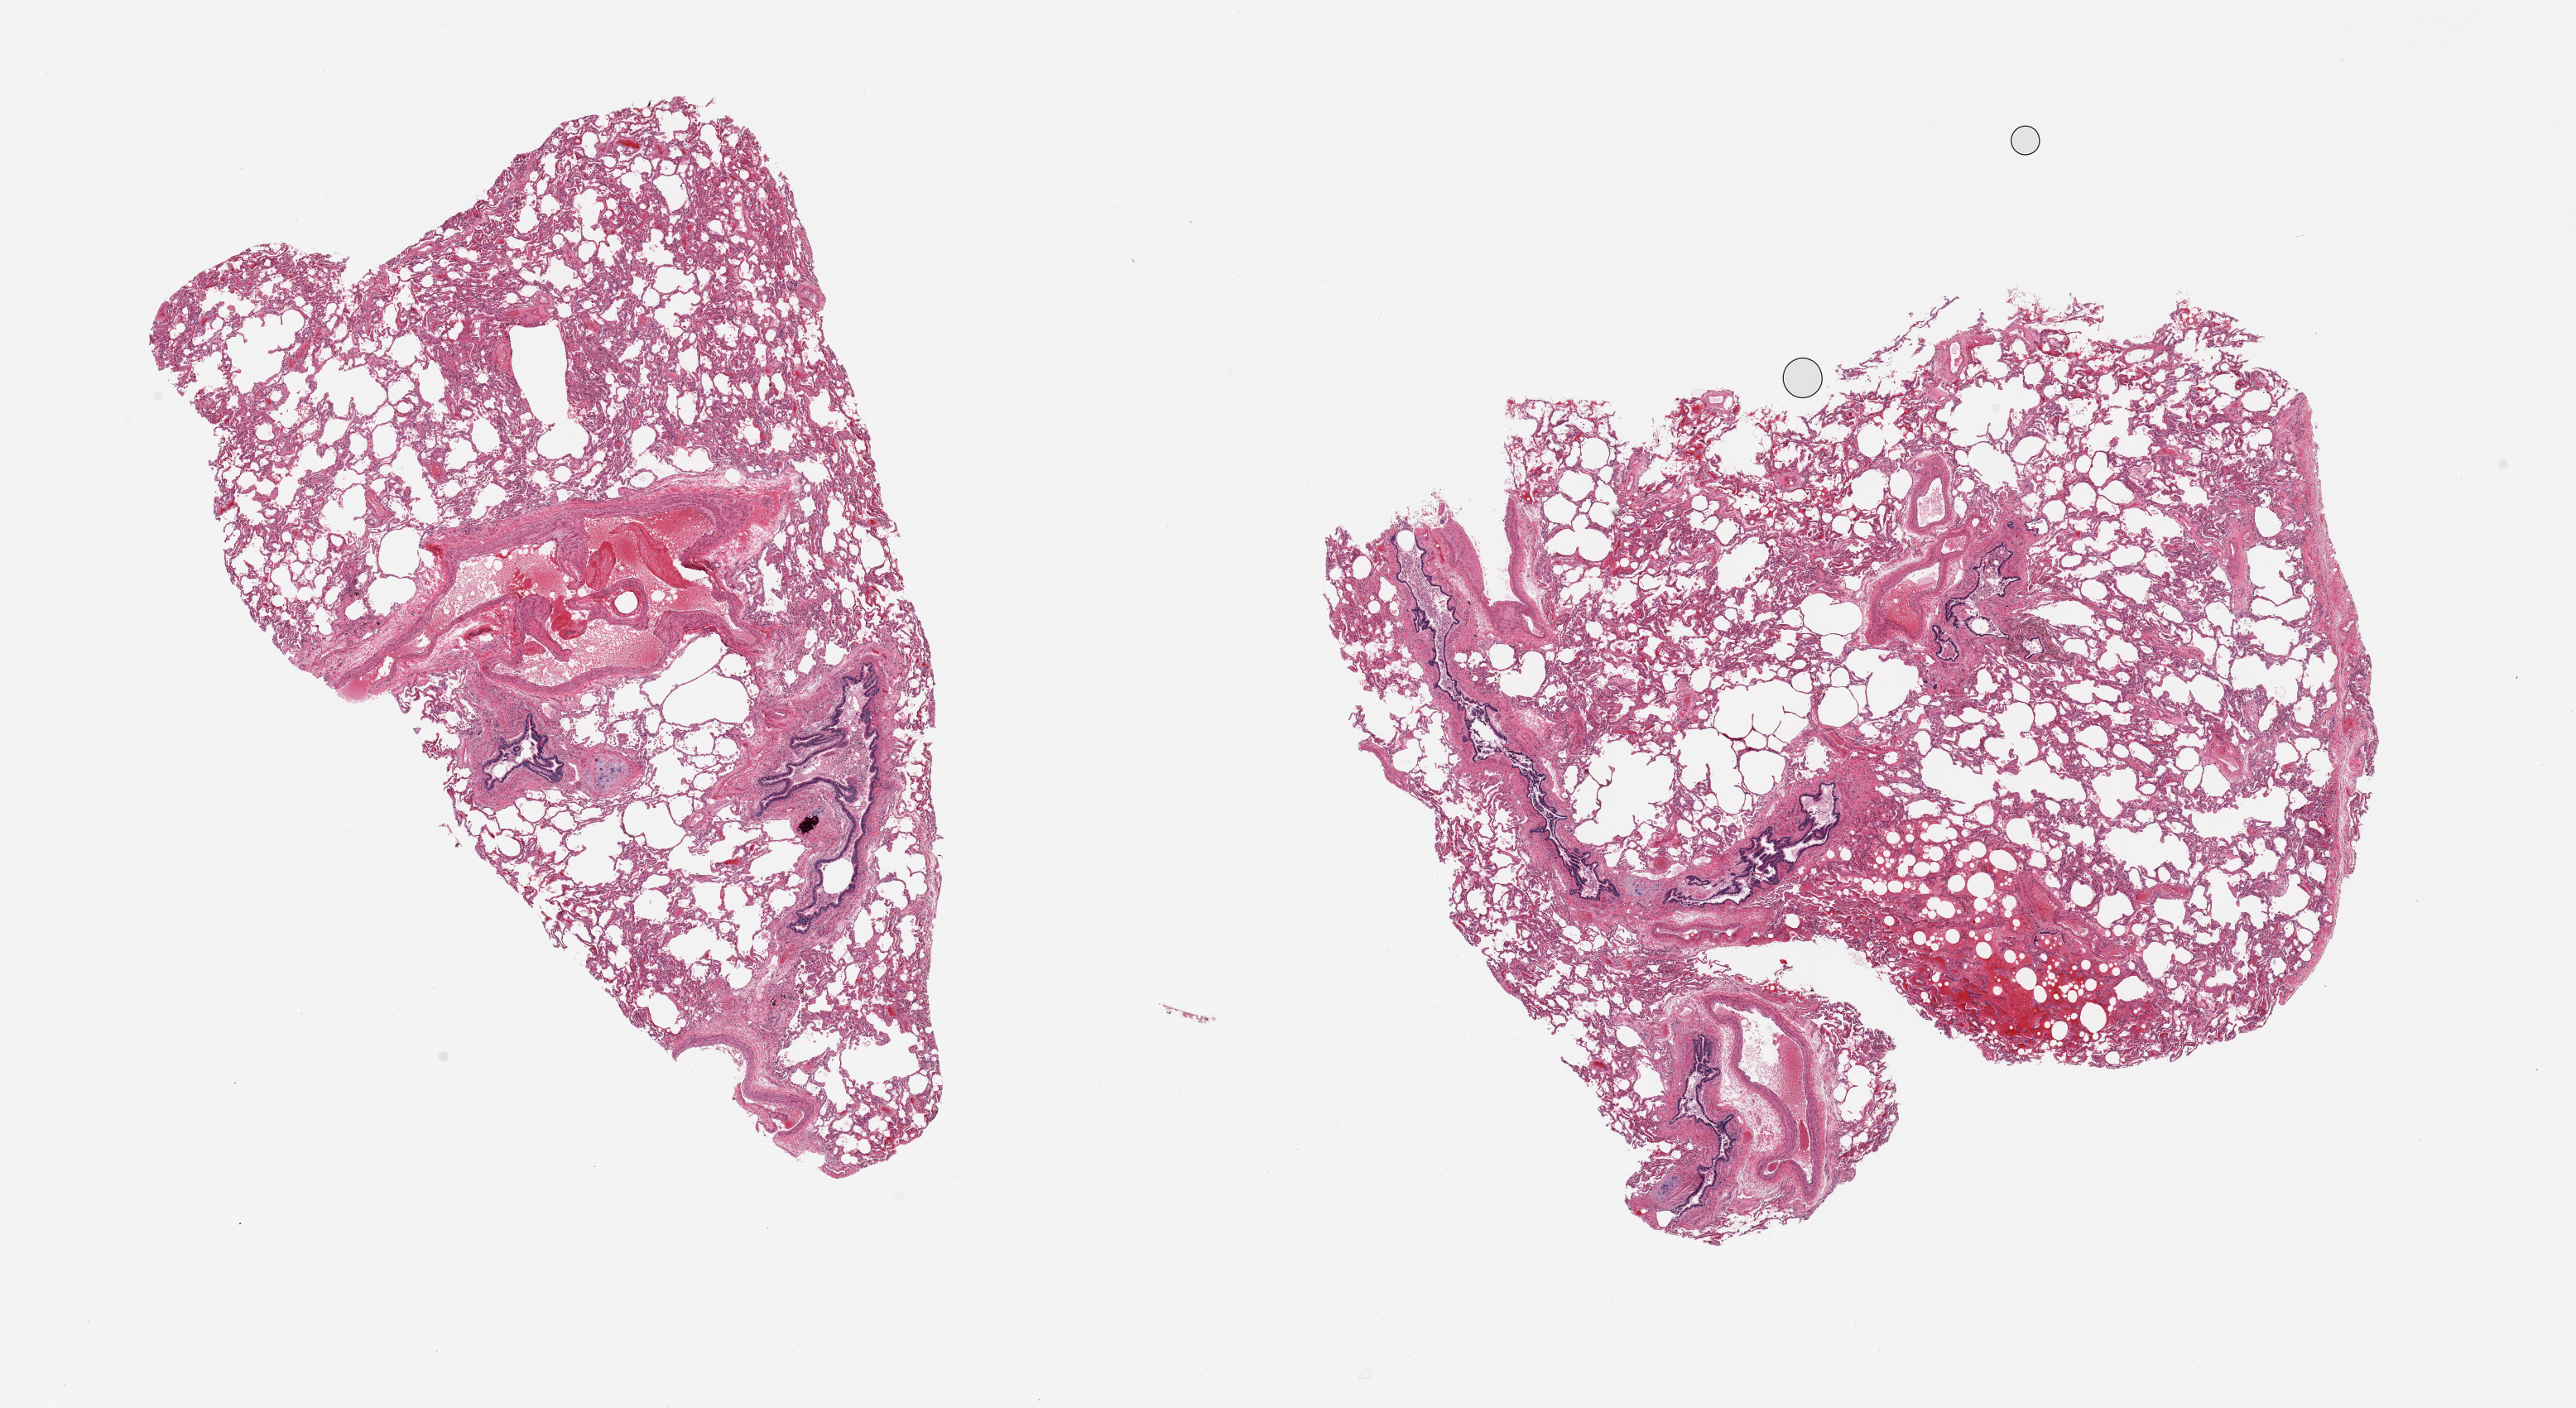
Whole-slide image, haematoxylin and eosin stain — shown as a low-resolution overview of the whole scanned area (about 24.6 x 13.5 mm, acquisition: 20x scan), PAXgene-fixed paraffin-embedded (PFPE) section, sampled site (target tissue): lung, tissue donor sample.
Review note (as recorded): 2 pieces; emphysematous change, several large vessels, bronchi and cartilage; focus of hemorrhage.